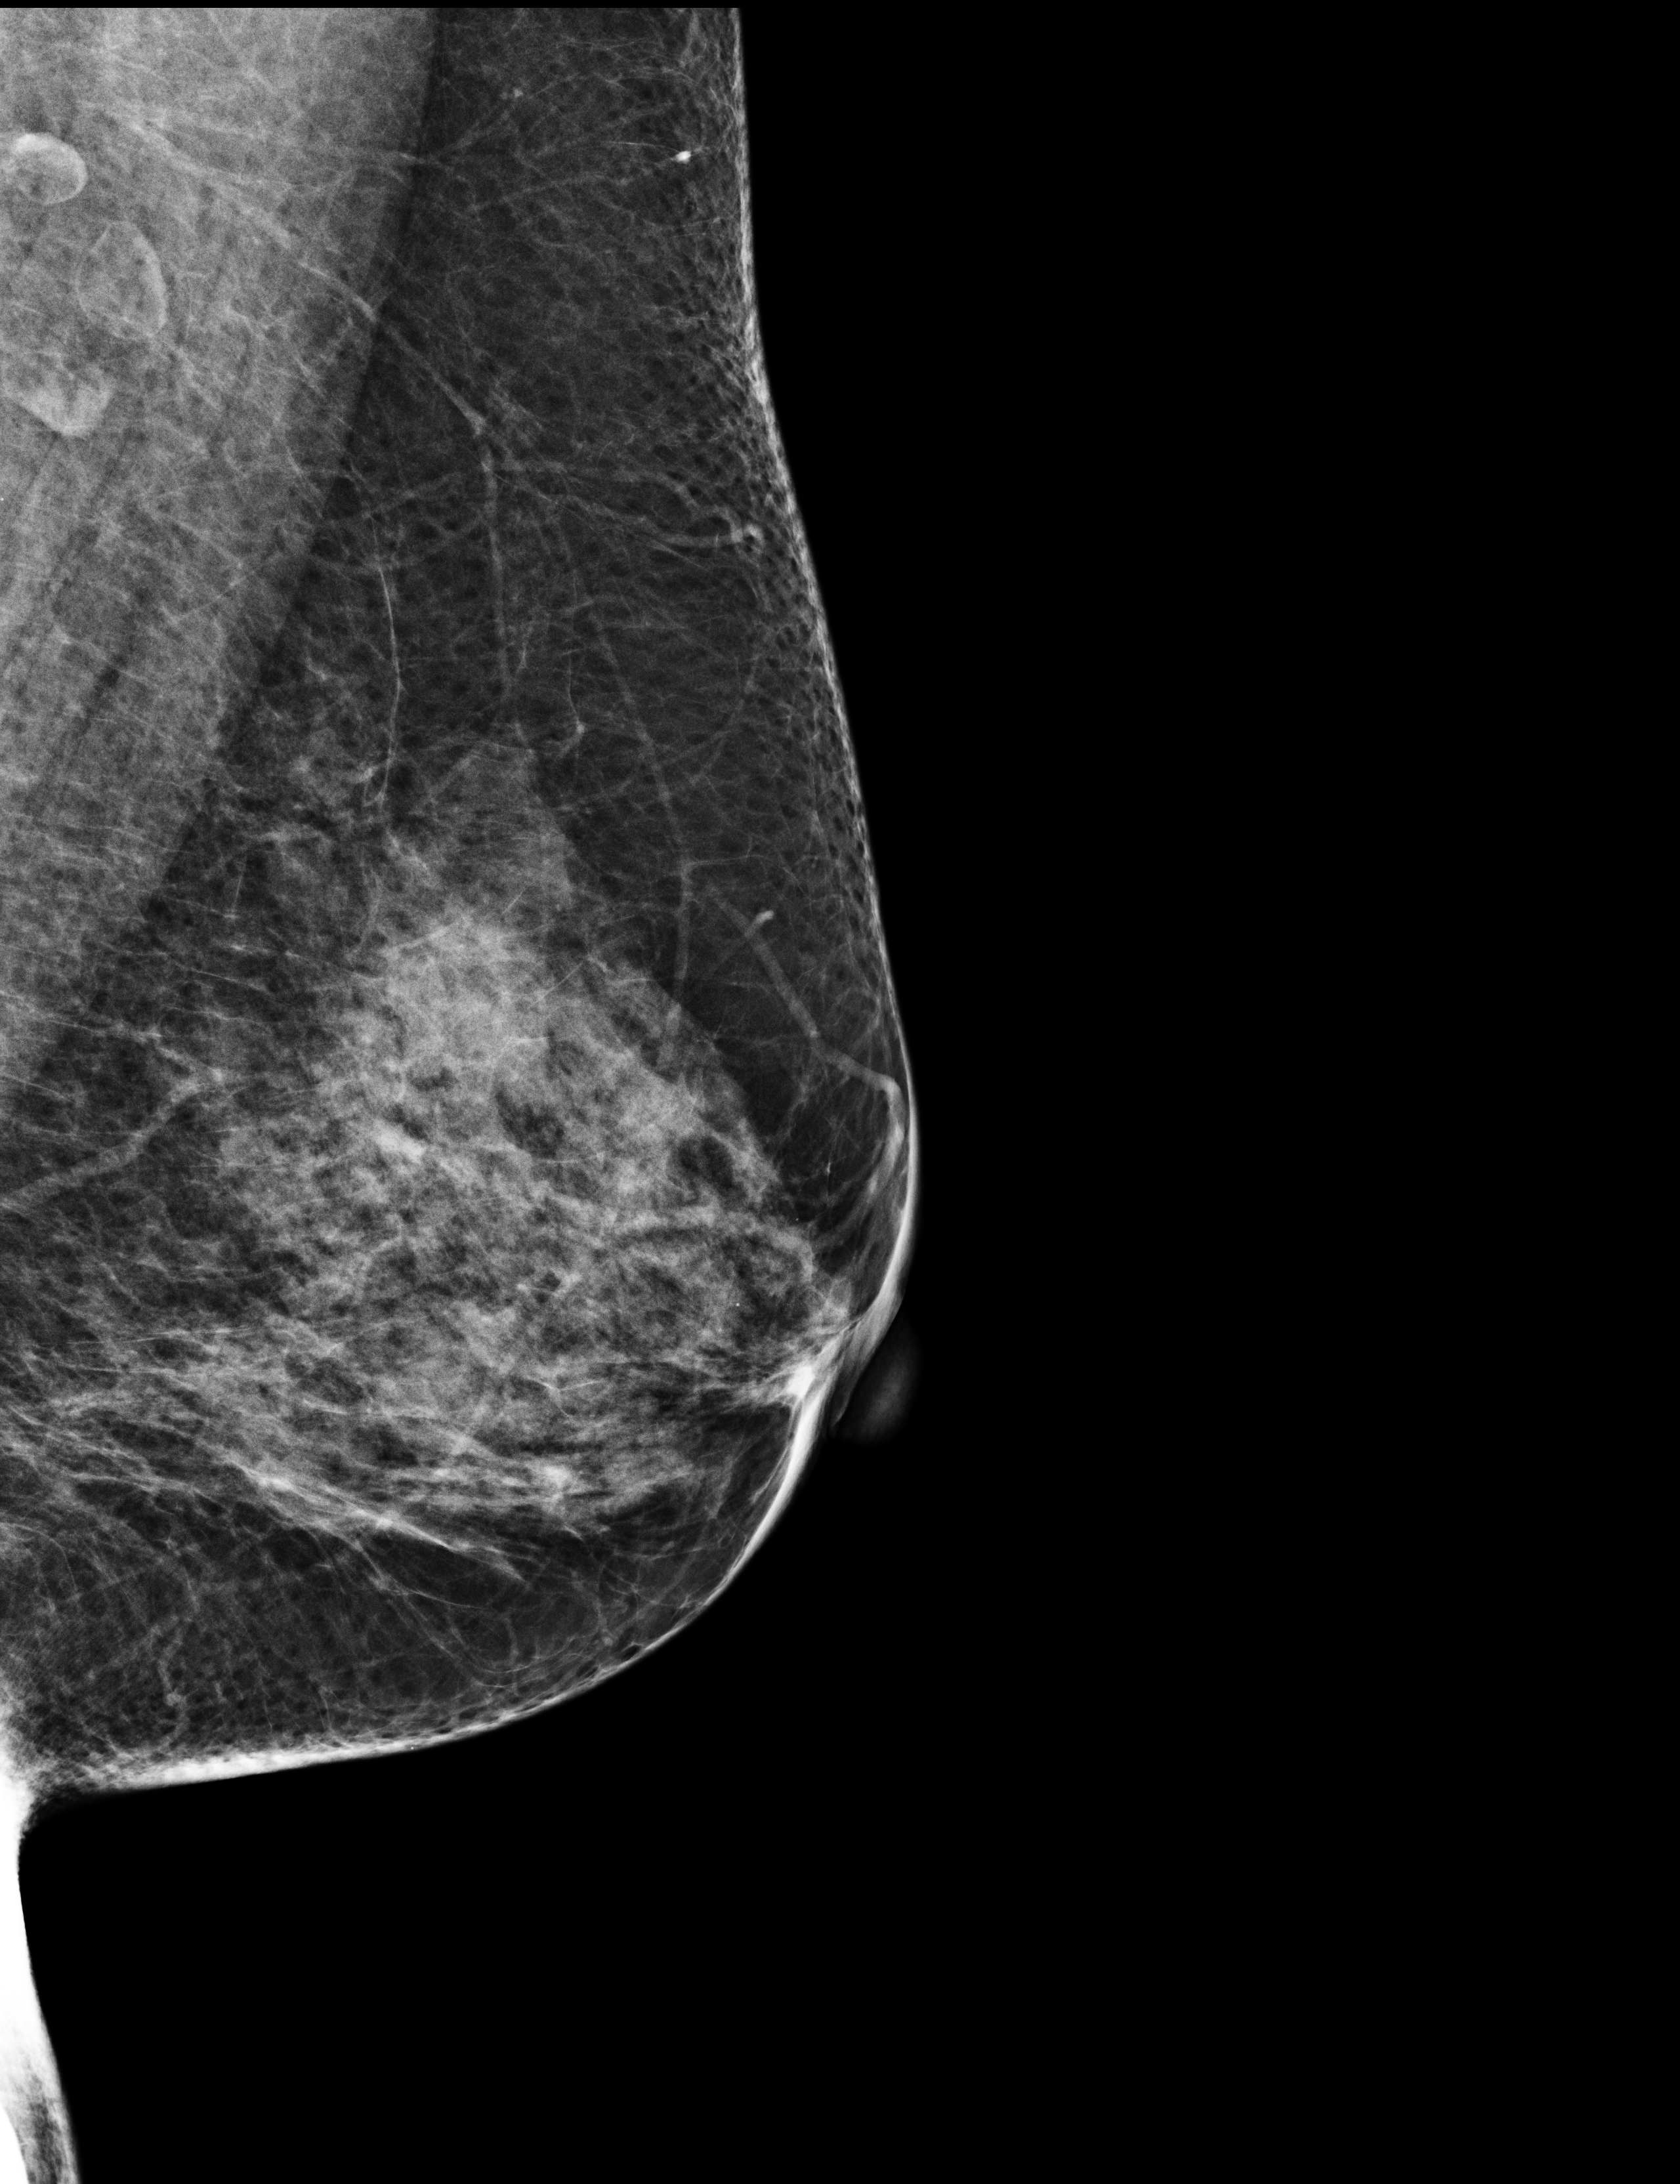
Screening examination. Patient aged 58 years (female).
Image type: full-field digital mammogram. Breast: left. Projection: medio-lateral oblique projection, infra-mammary fold.